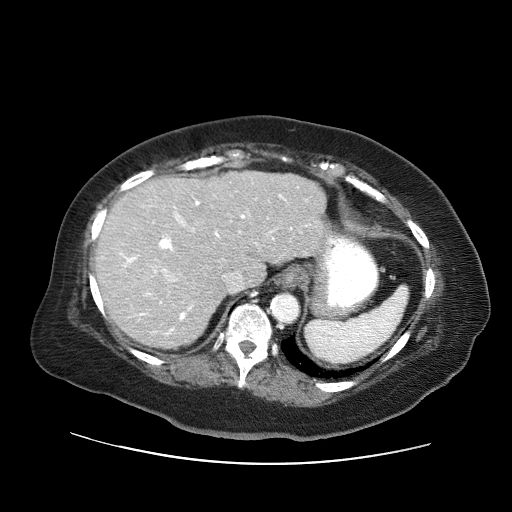
Contrast-enhanced abdominal CT (liver protocol), one axial slice. Position 43 of 71 along the scan axis. Reconstruction kernel STANDARD. Soft-tissue window (W 400 / L 40 HU). 512 × 512 image matrix, field of view 400 × 400 mm. From the clinical record (not read from this slice): diagnosis: hepatocellular carcinoma (patient treated with transarterial chemoembolisation; whether this scan precedes or follows treatment is not stated here); TNM stage (as recorded): Stage-II; Child-Pugh class: A; tumour nodularity: multinodular; tumour size: 5 cm.
Annotated regions visible in this slice (semi-automatically segmented with operator editing):
- liver parenchyma outside the tumour (the mass and vessels are separate outlines, so this box may not span the whole liver): bounding box <94,170,332,348> (left, top, right, bottom; pixels)
- liver vessels: <119,194,310,335>